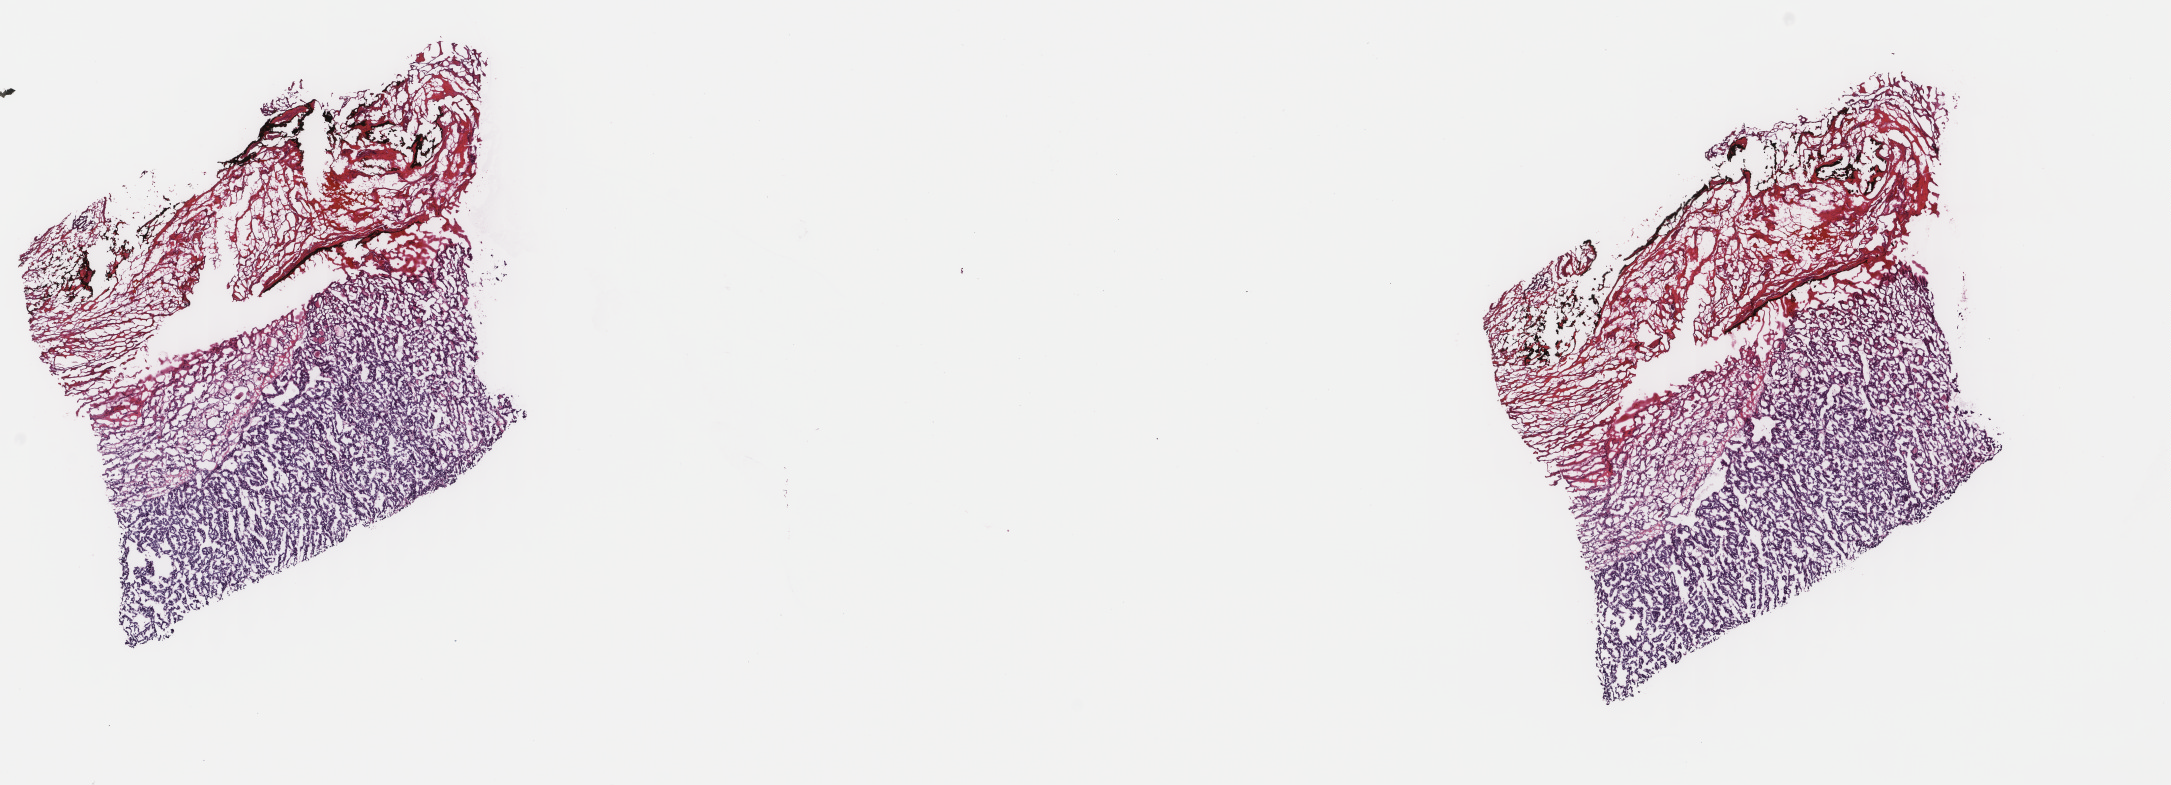
Whole-slide histology image, Hematoxylin and eosin (H&E) stained, whole scanned area (about 17.2 x 6.2 mm) shown as a low-resolution overview, frozen section from the top of the tissue portion, sample: primary tumour, thyroid. Female, age 35 years at initial diagnosis. Pathologist review of this section (percent, as recorded): tumour cells 55%, tumour nuclei 75%, normal cells 45%, stromal cells 0%, necrosis 0%. Inflammatory infiltration, as recorded: lymphocyte infiltration 0%, monocyte infiltration 0%, neutrophil infiltration 0%.
Diagnosis: Papillary adenocarcinoma, NOS (thyroid gland). Laterality: right. TNM: T3 NX MX. AJCC pathologic stage: I.